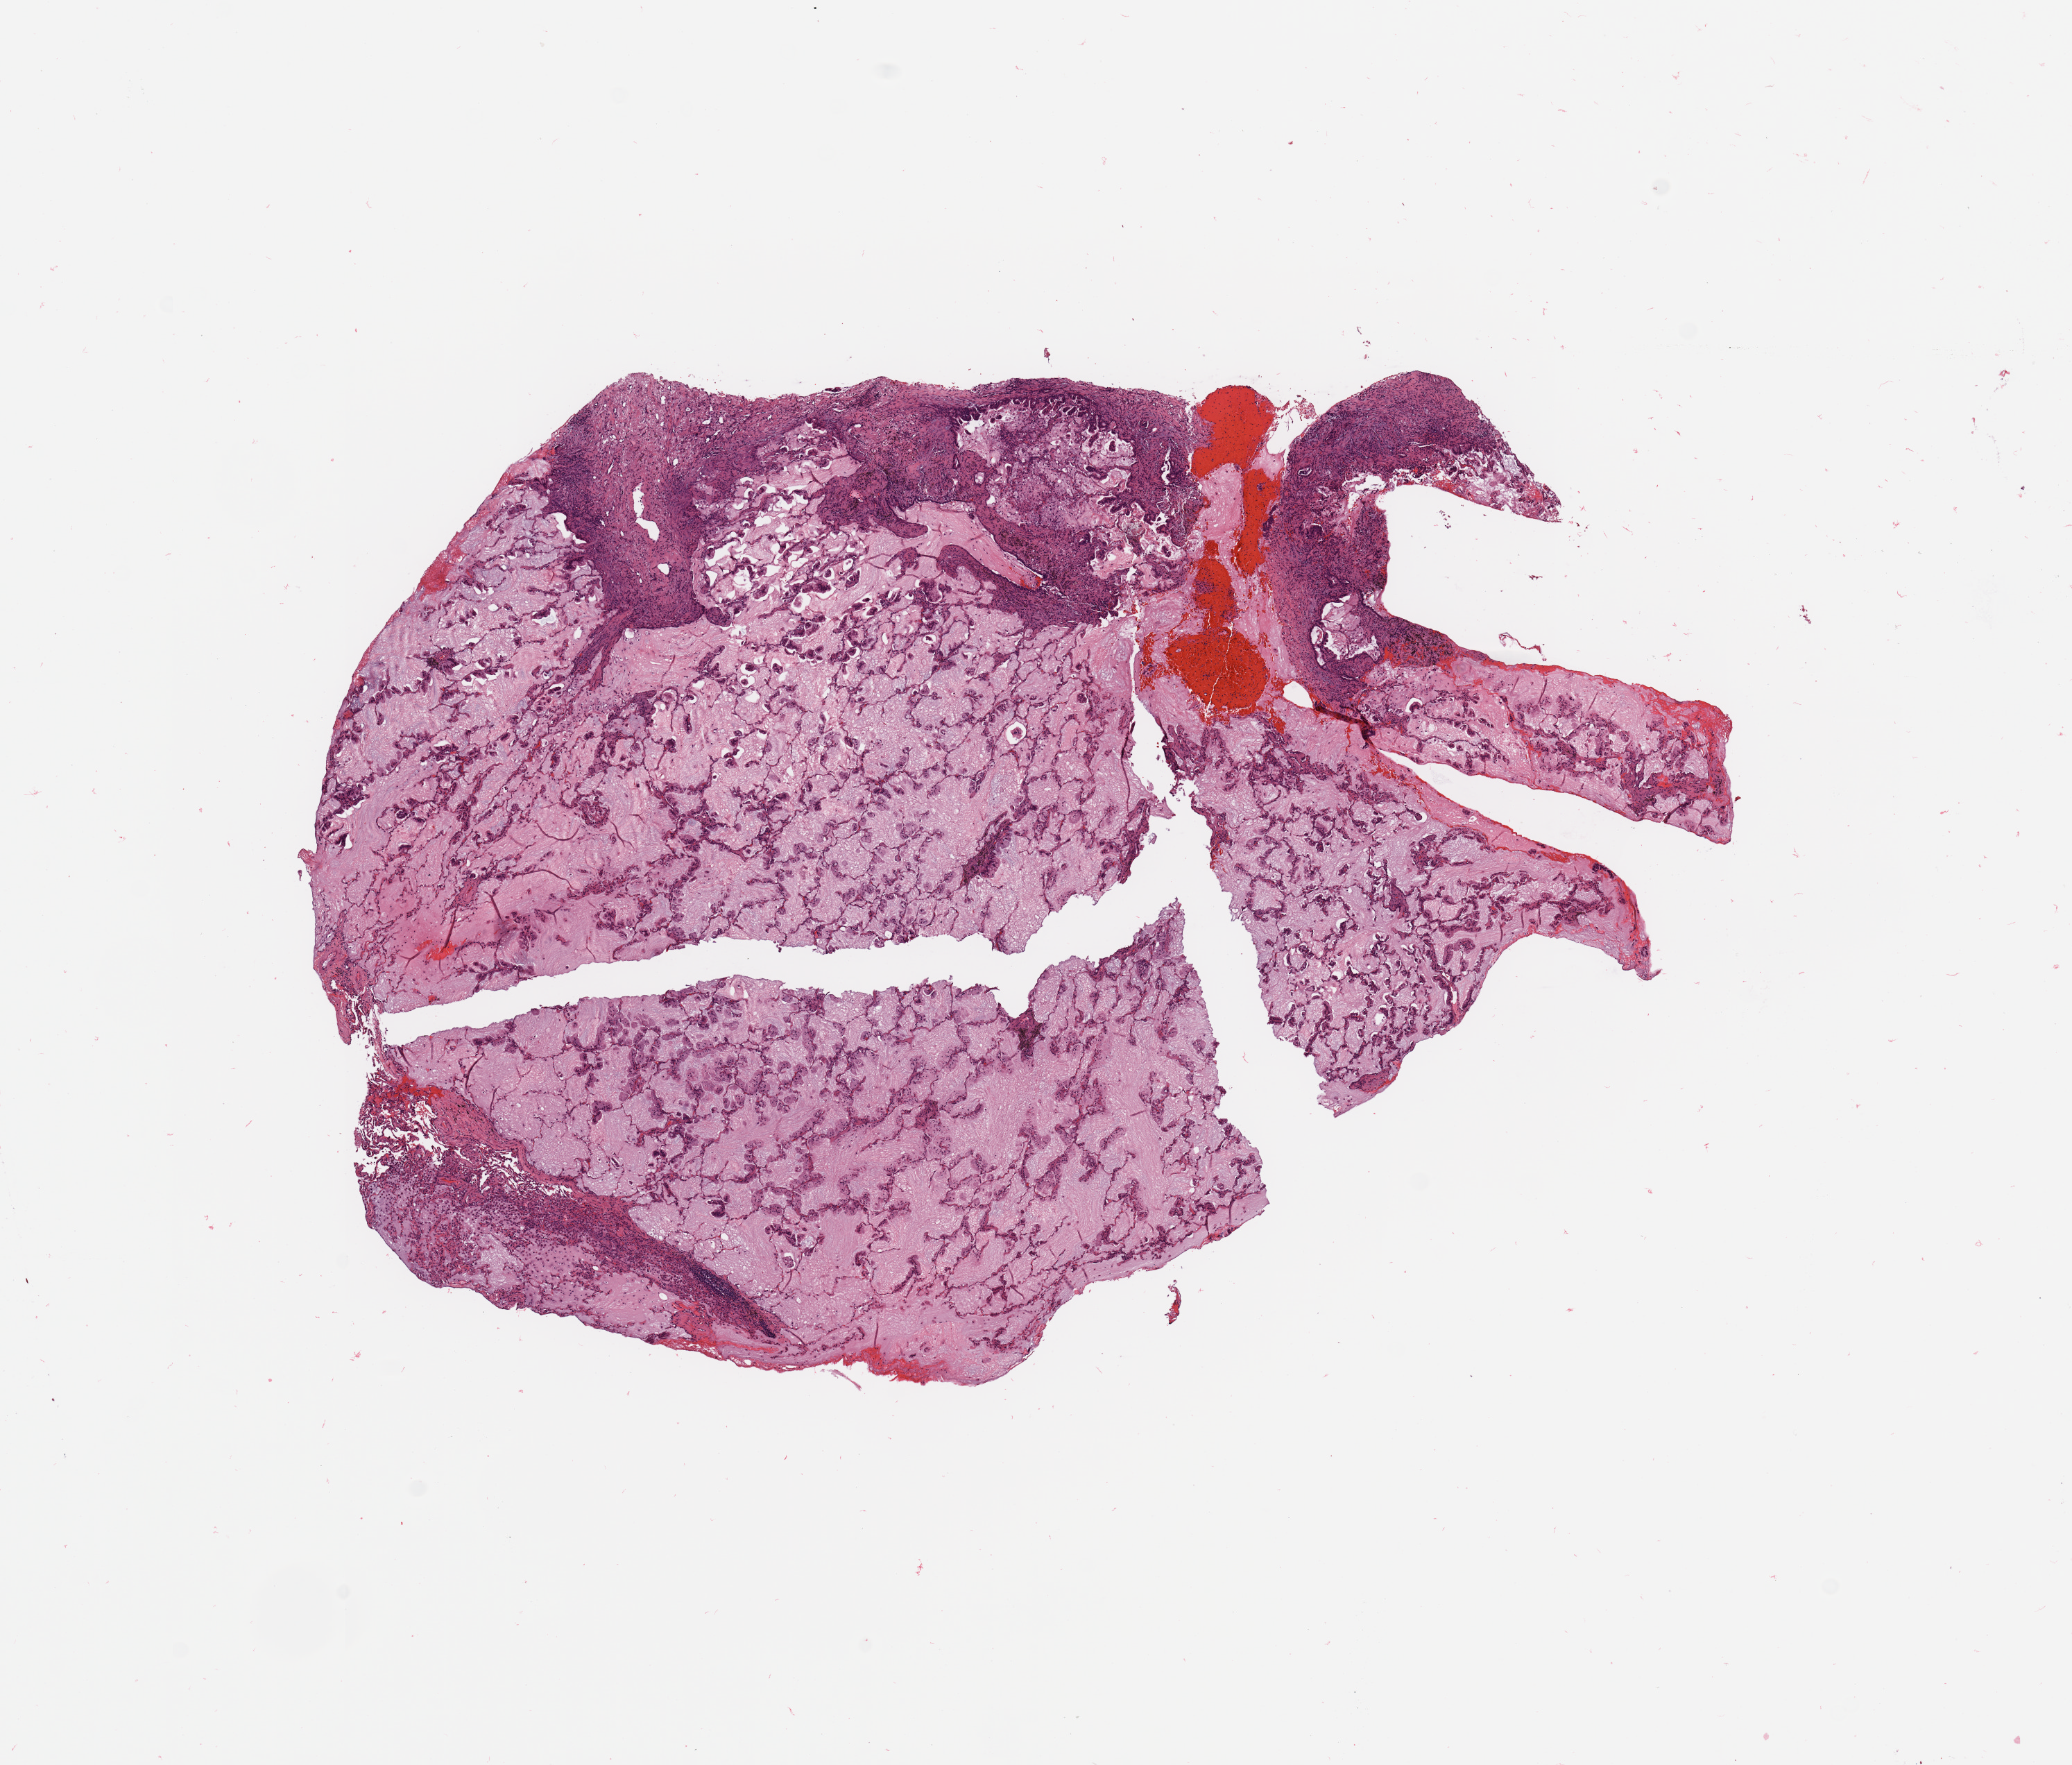
Digitized Hematoxylin and eosin (H&E) stained tissue section (whole slide), a low-resolution overview of the entire scanned area, about 11.8 x 10.1 mm, tumour tissue sample, sampled site: lung. Male, 65 y/o. Histologic grade: G2 (moderately differentiated). Composition of this section per pathologist review: tumour nuclei 60%, necrosis 0%.
* diagnosis: Adenocarcinoma, NOS
* primary tumour site (as recorded): left upper lobe
* AJCC pathologic stage: IB